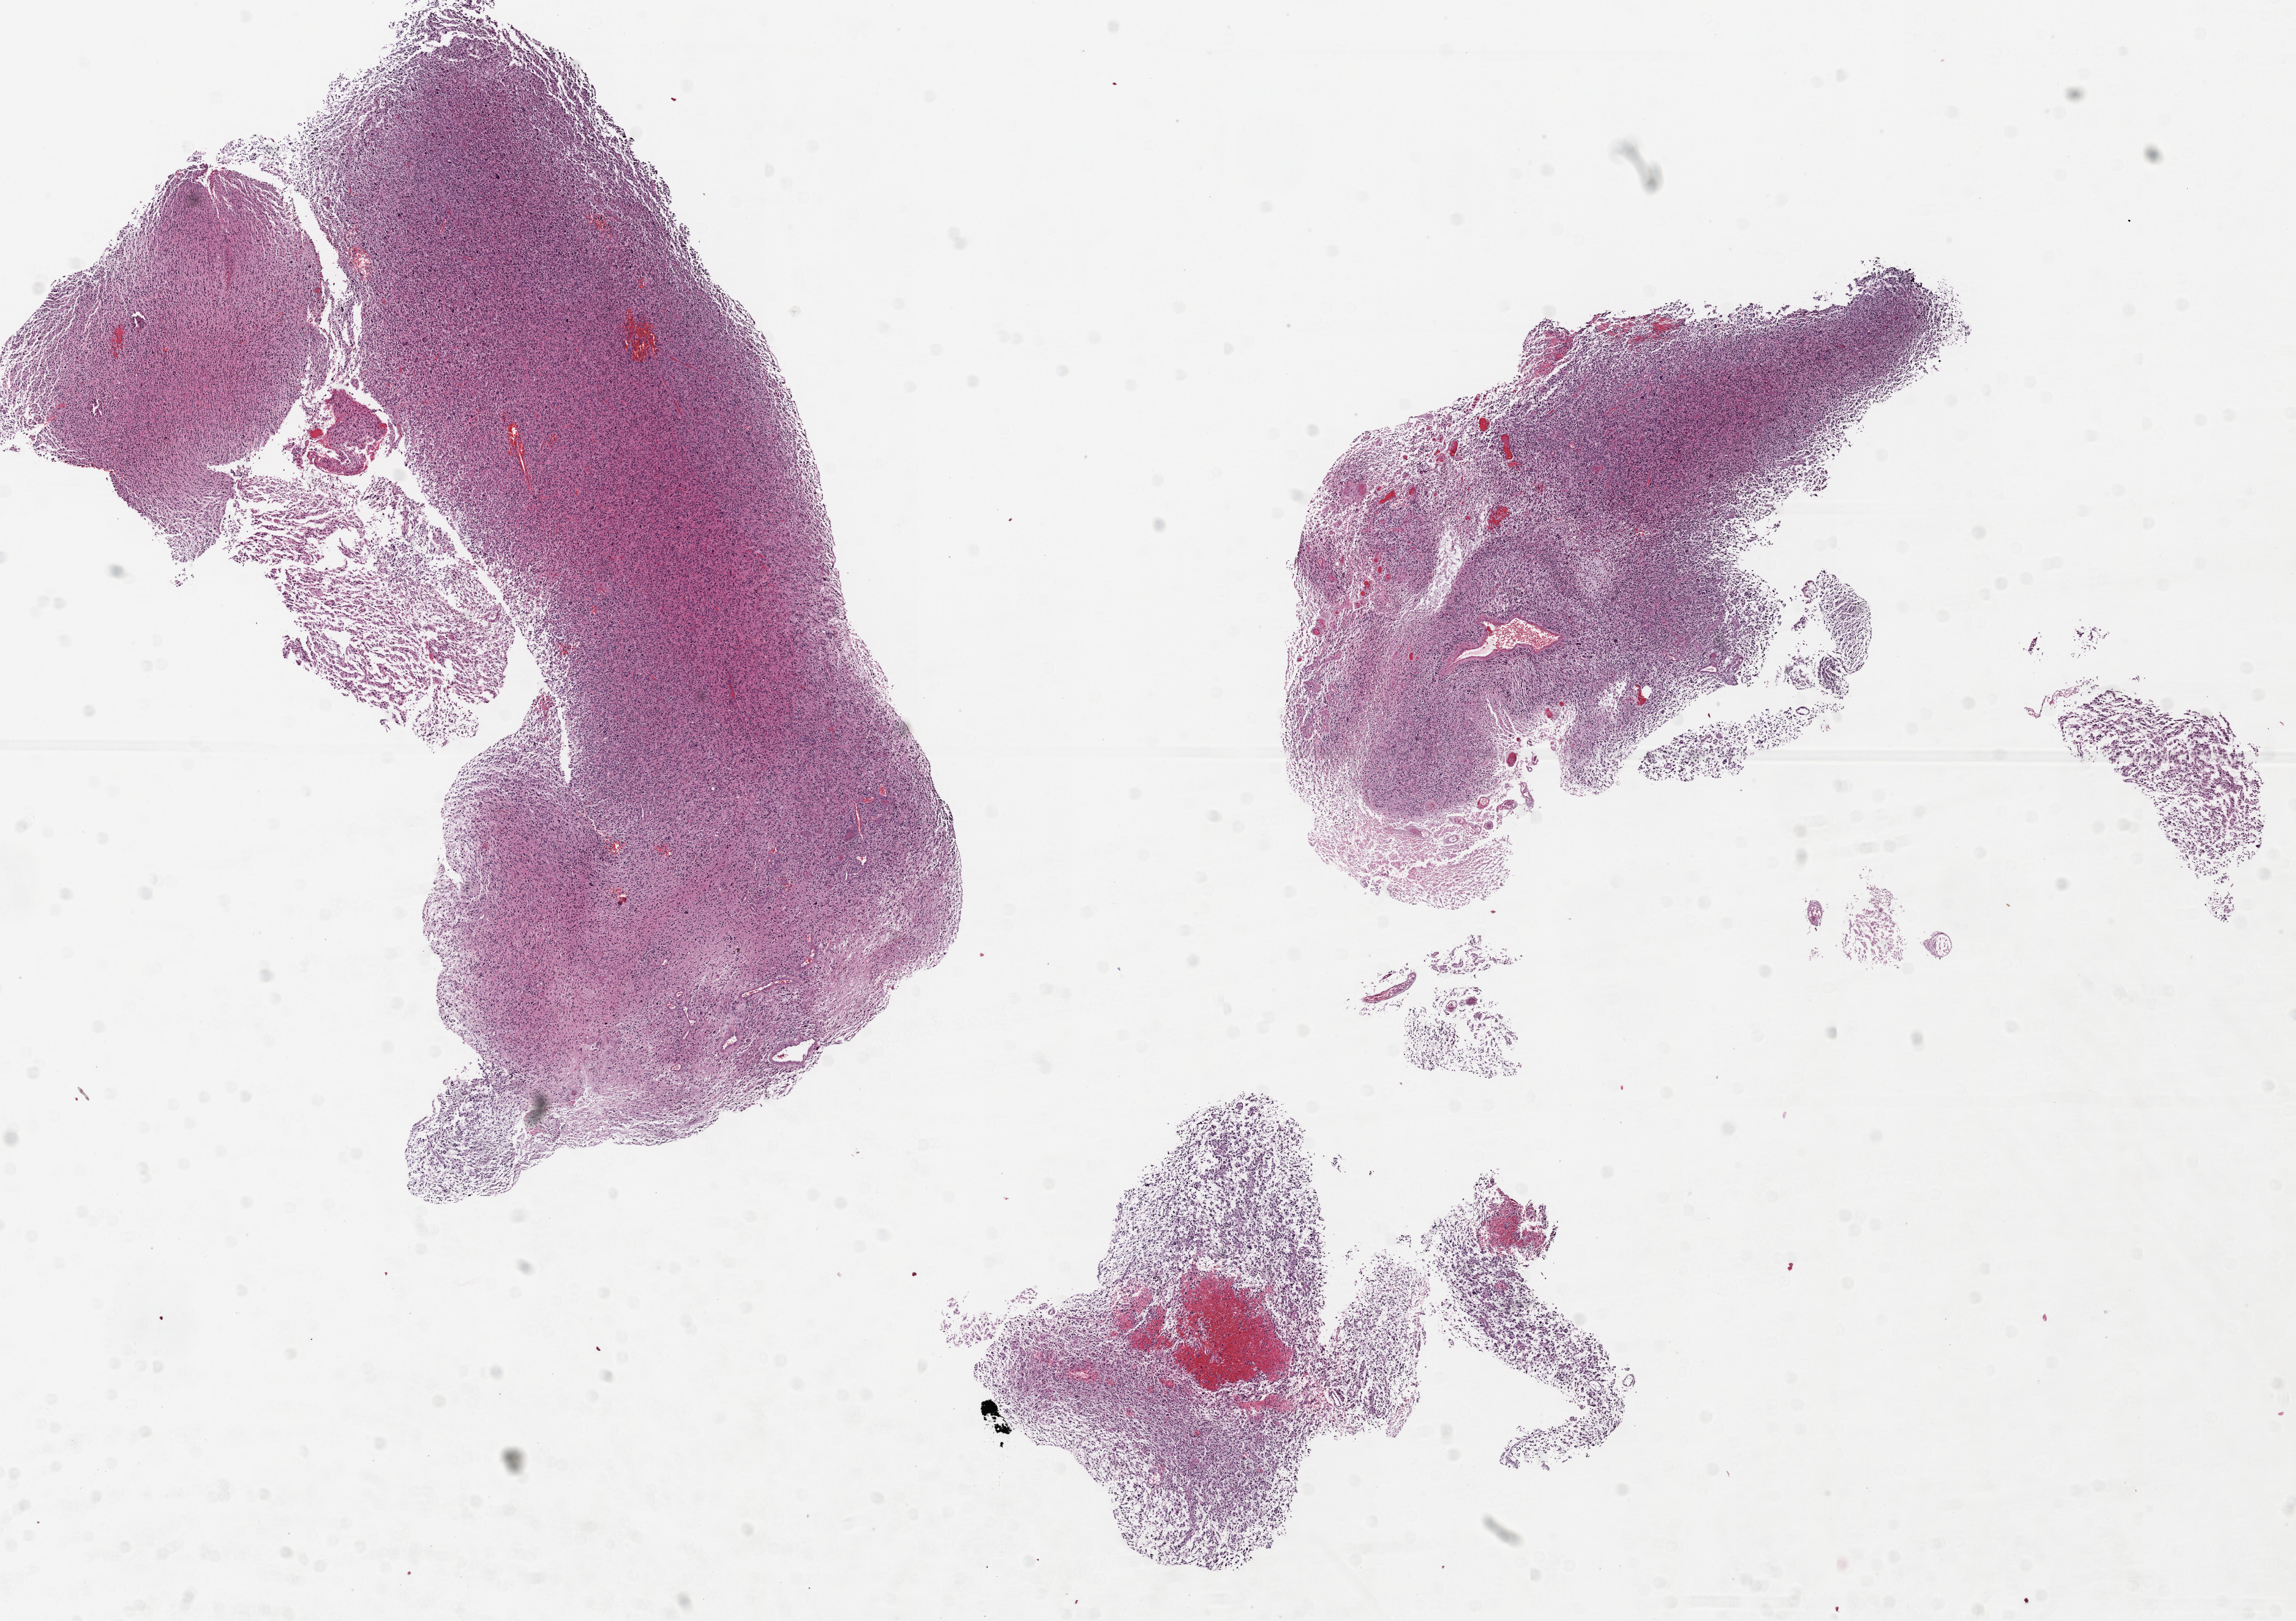
Whole-slide histology image, H&E — whole scanned area (about 15.0 x 10.6 mm) shown as a low-resolution overview, FFPE section, sample: primary tumour, brain. Male, age 69 years at initial diagnosis.
* pathologic diagnosis: Glioblastoma